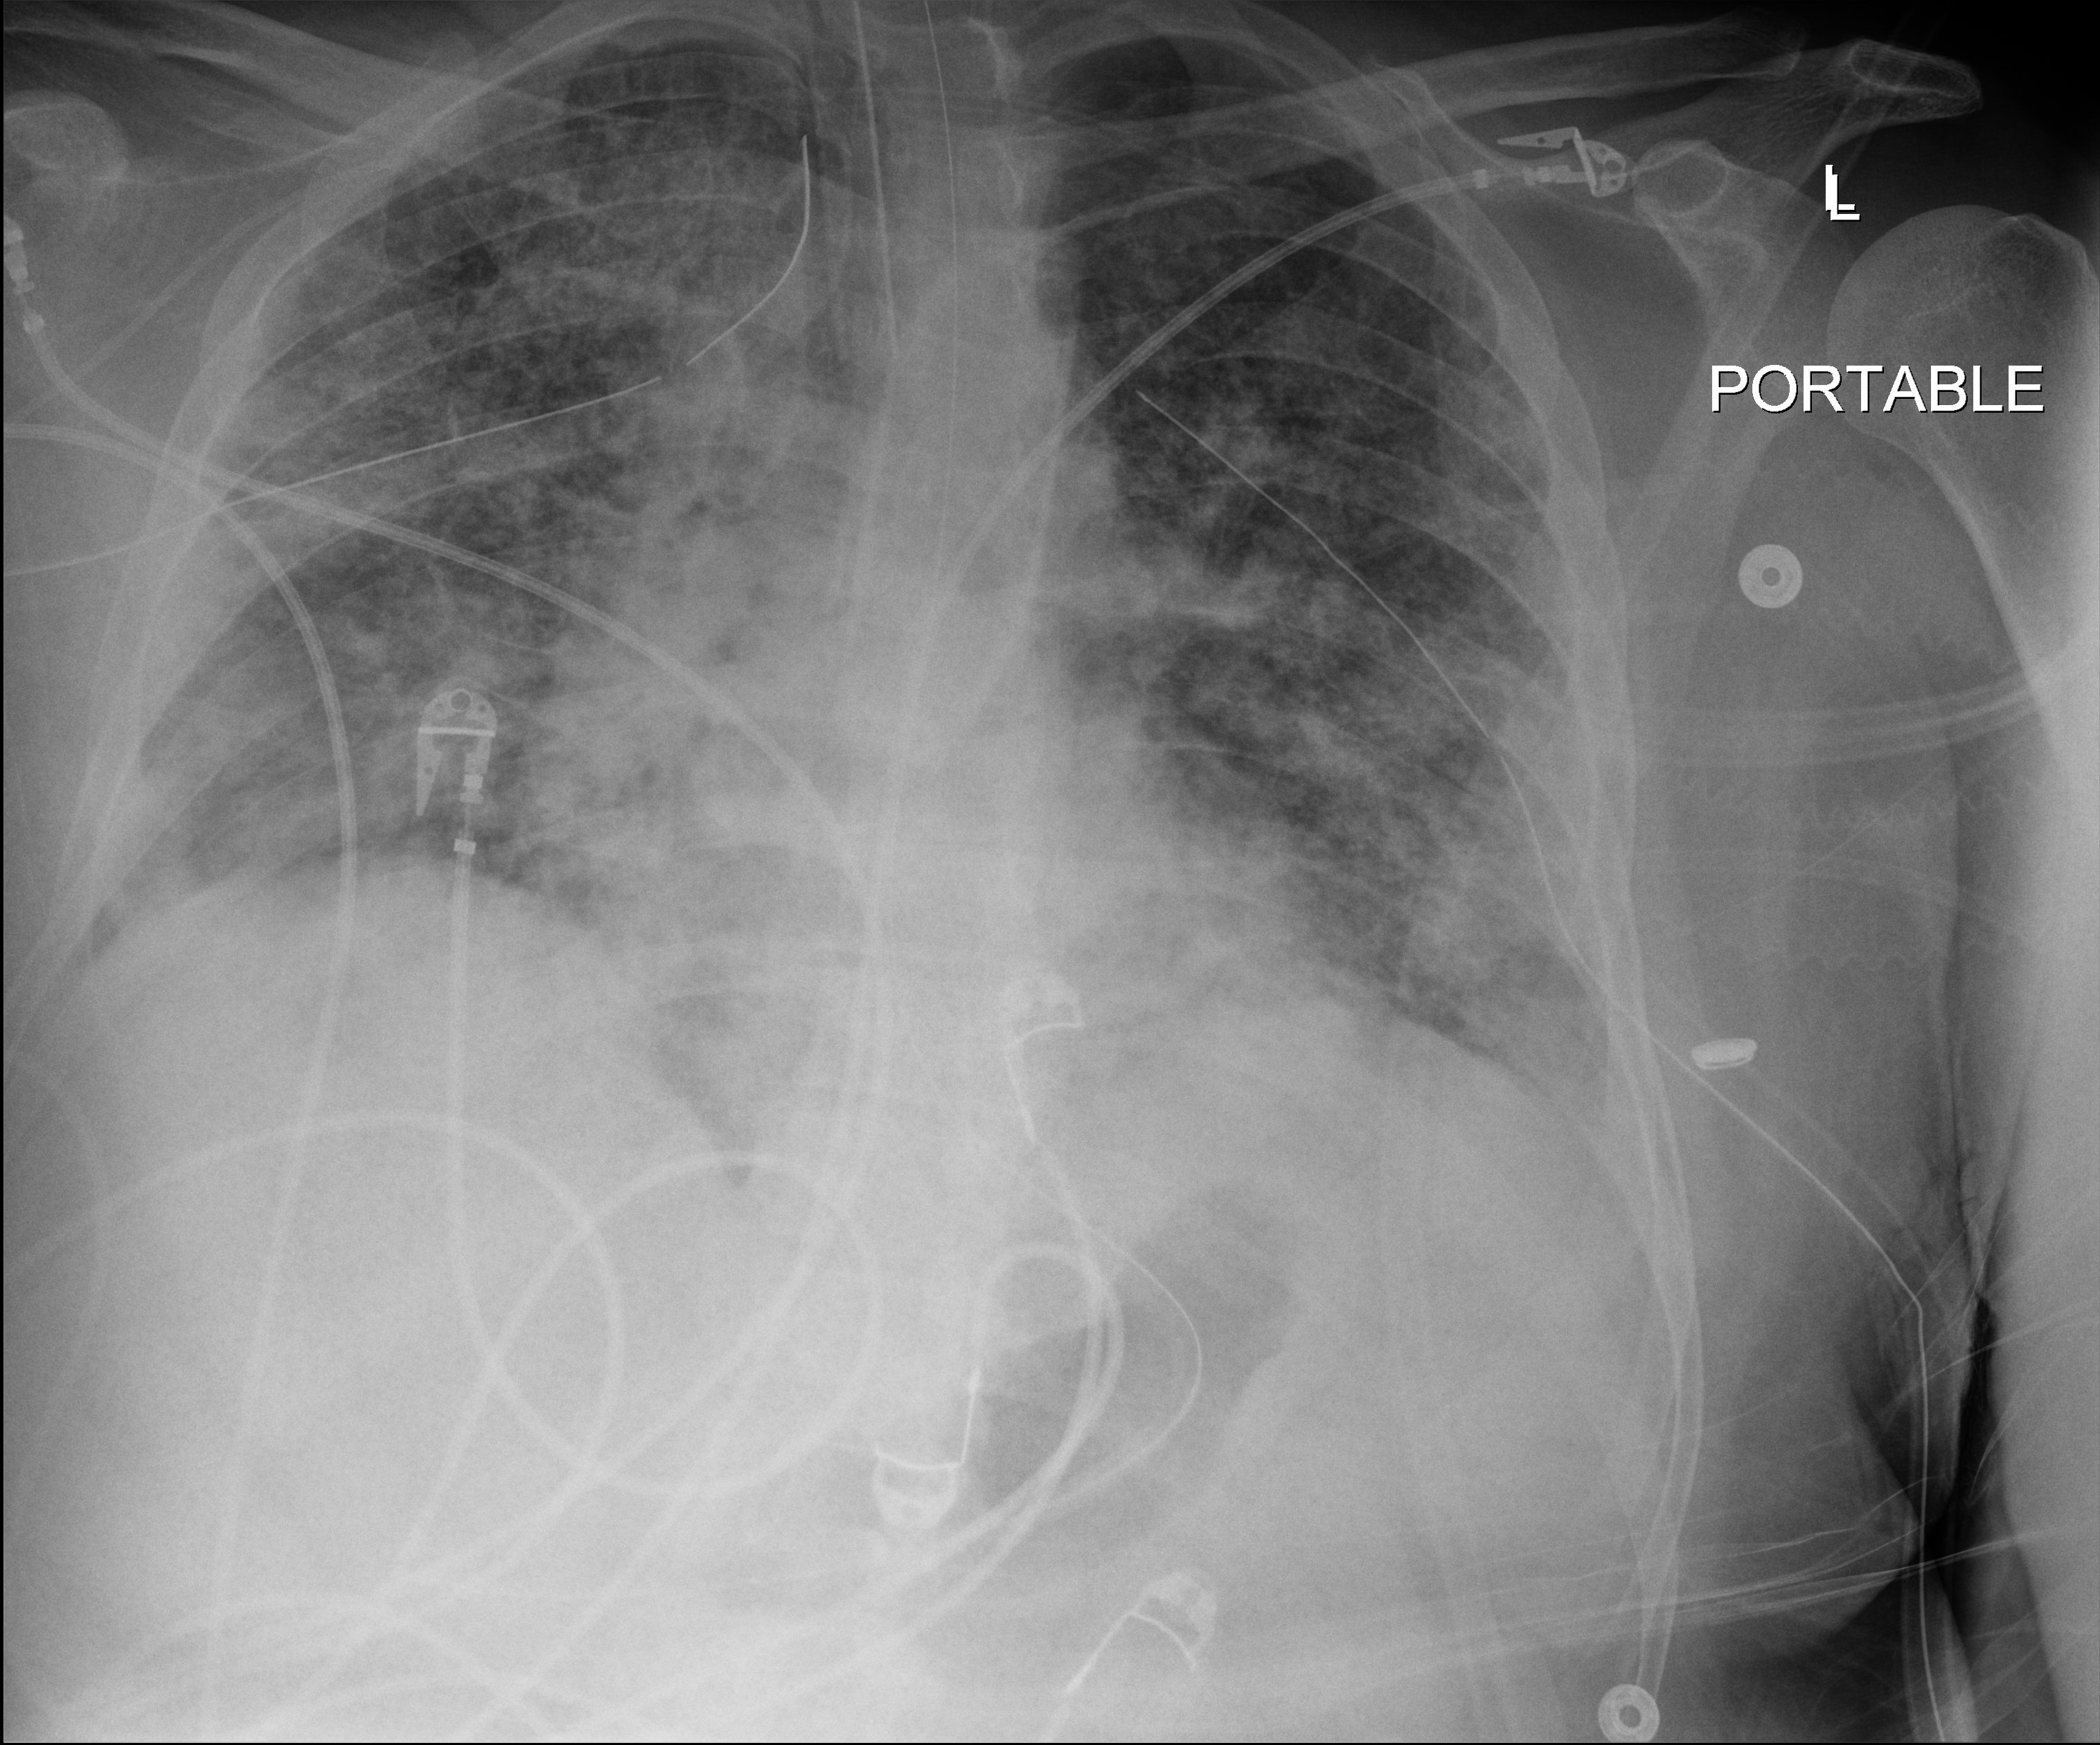
Chest radiograph; anteroposterior (AP) projection. Male patient hospitalised with COVID-19, age 18–59 years.
Hospital-stay facts (about this admission, not read from this image; timing relative to this image not recorded): admitted to intensive care during this hospital stay: yes.